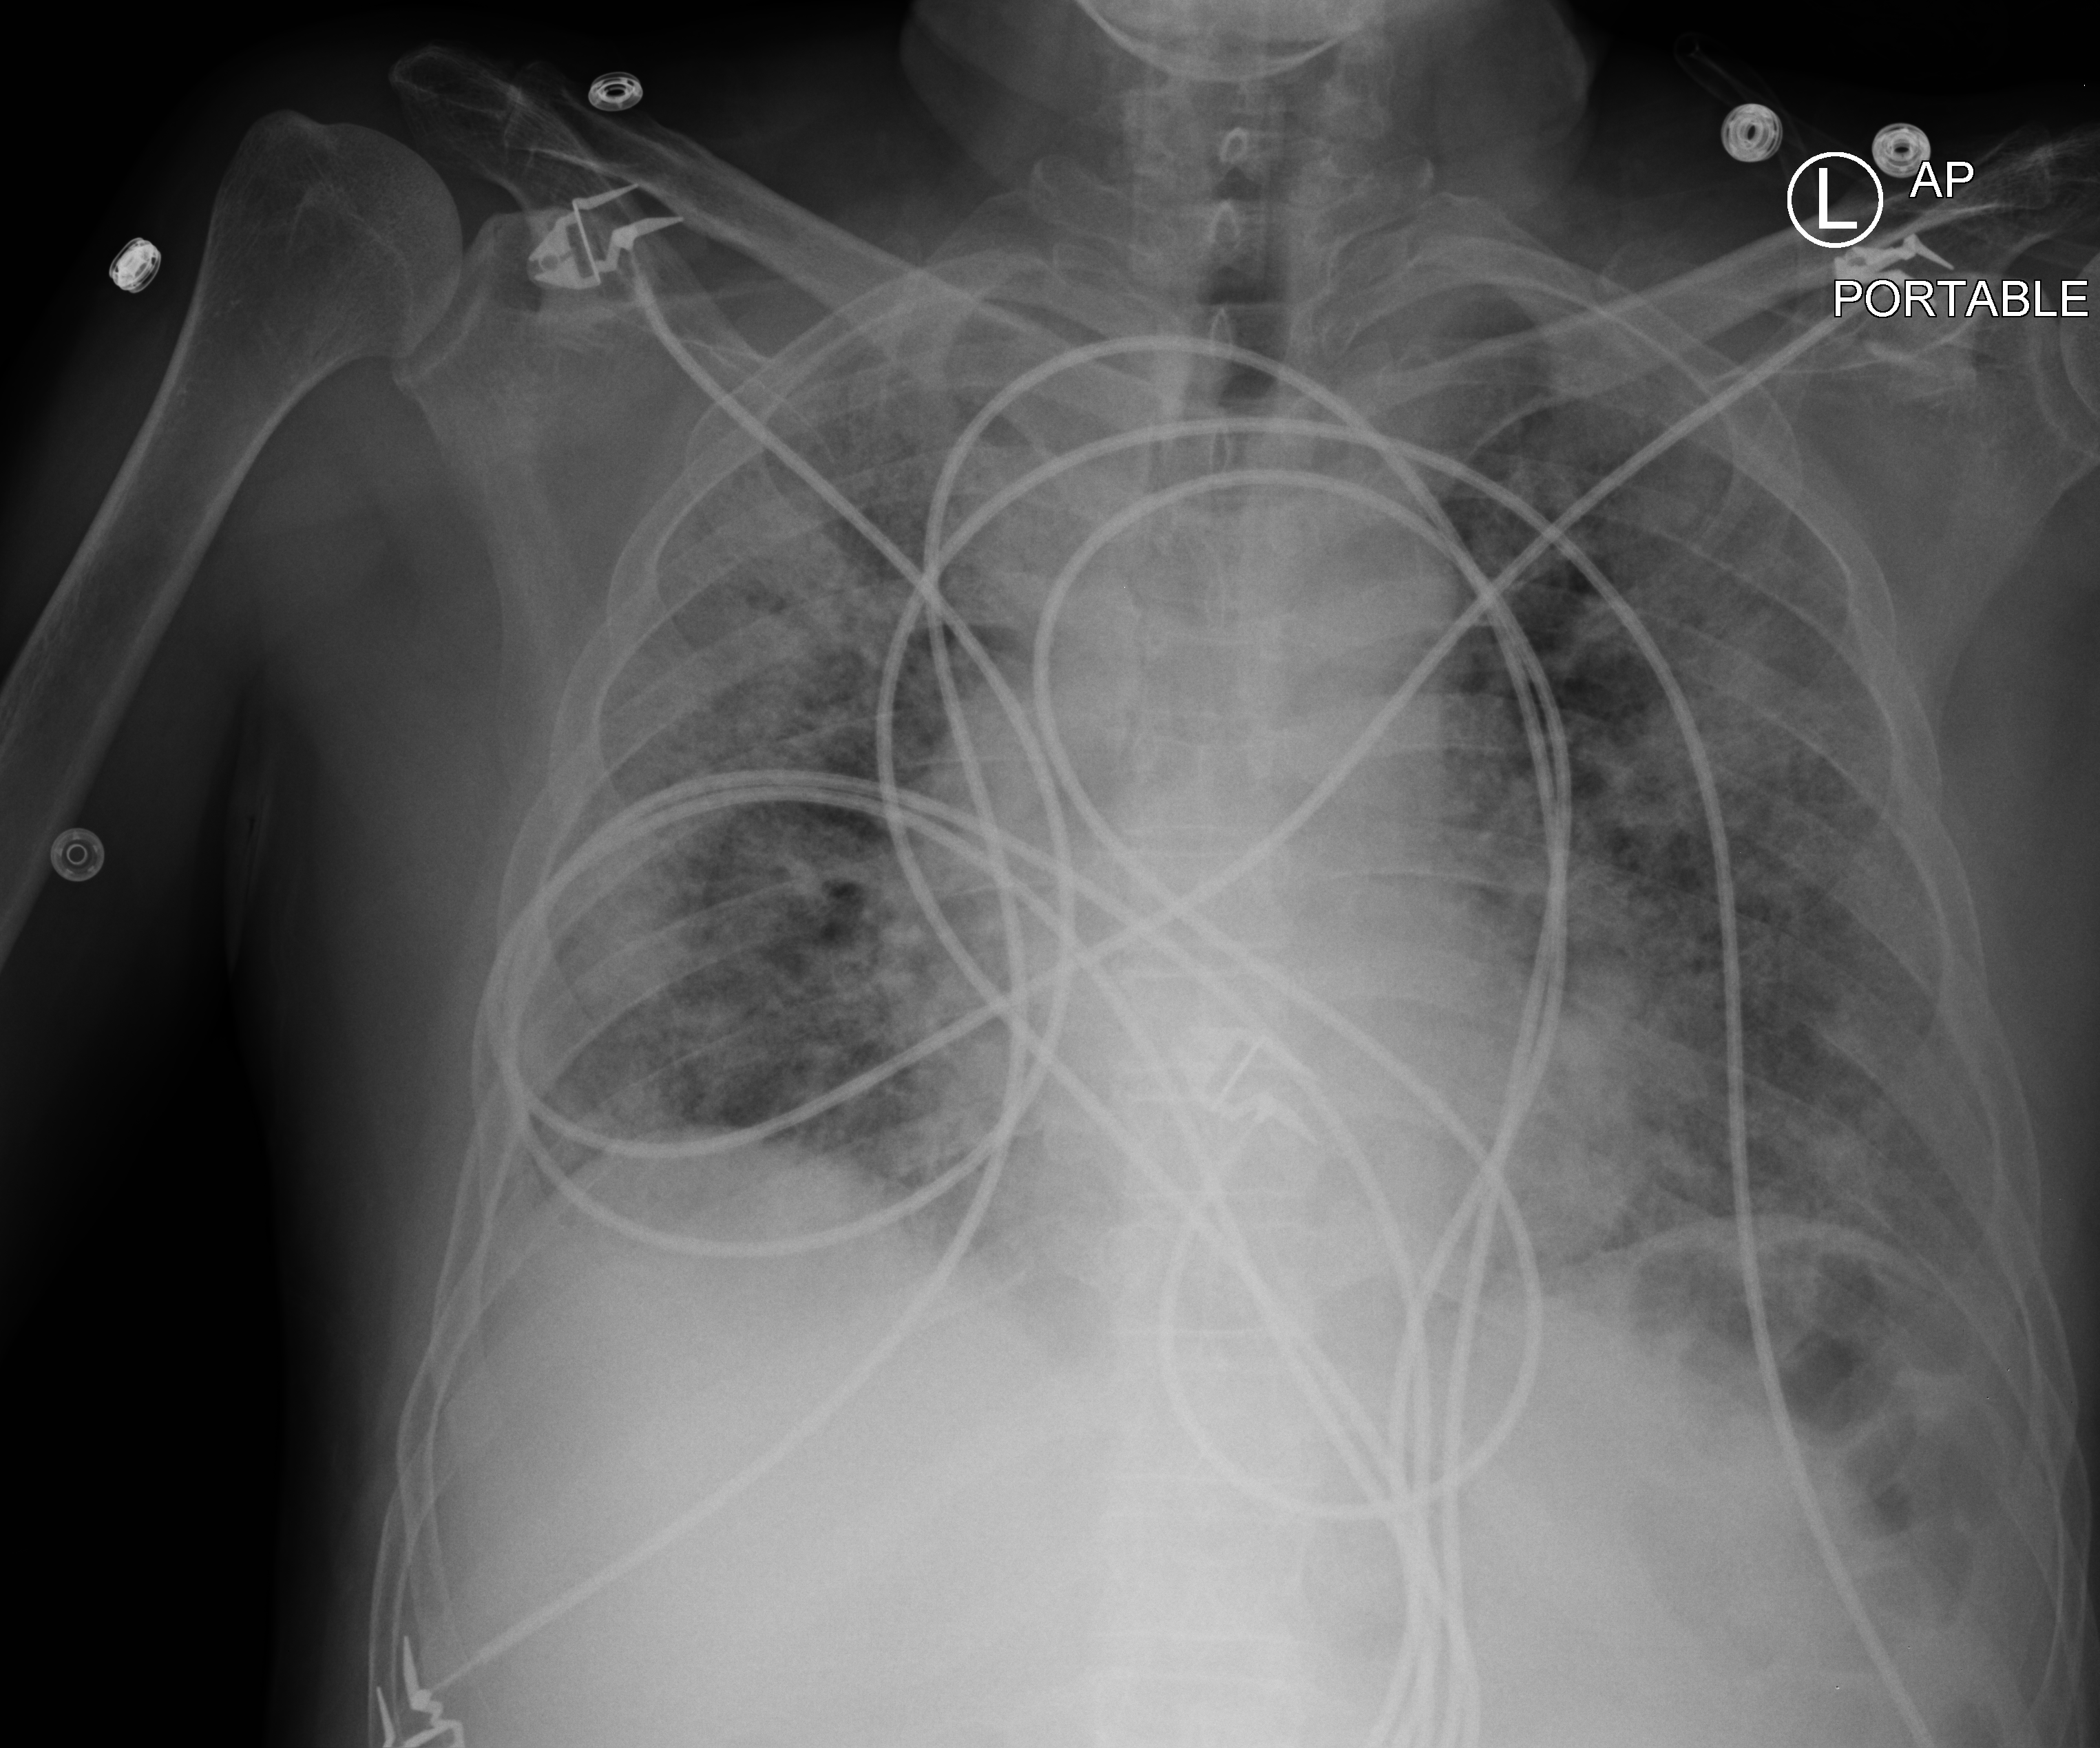
Portable chest radiograph; anteroposterior (AP) projection. Patient hospitalised with COVID-19; male, aged 60–74 years.
Hospital-stay facts (about this admission, not read from this image; timing relative to this image not recorded): mechanically ventilated during this hospital stay: yes; admitted to intensive care during this hospital stay: yes.